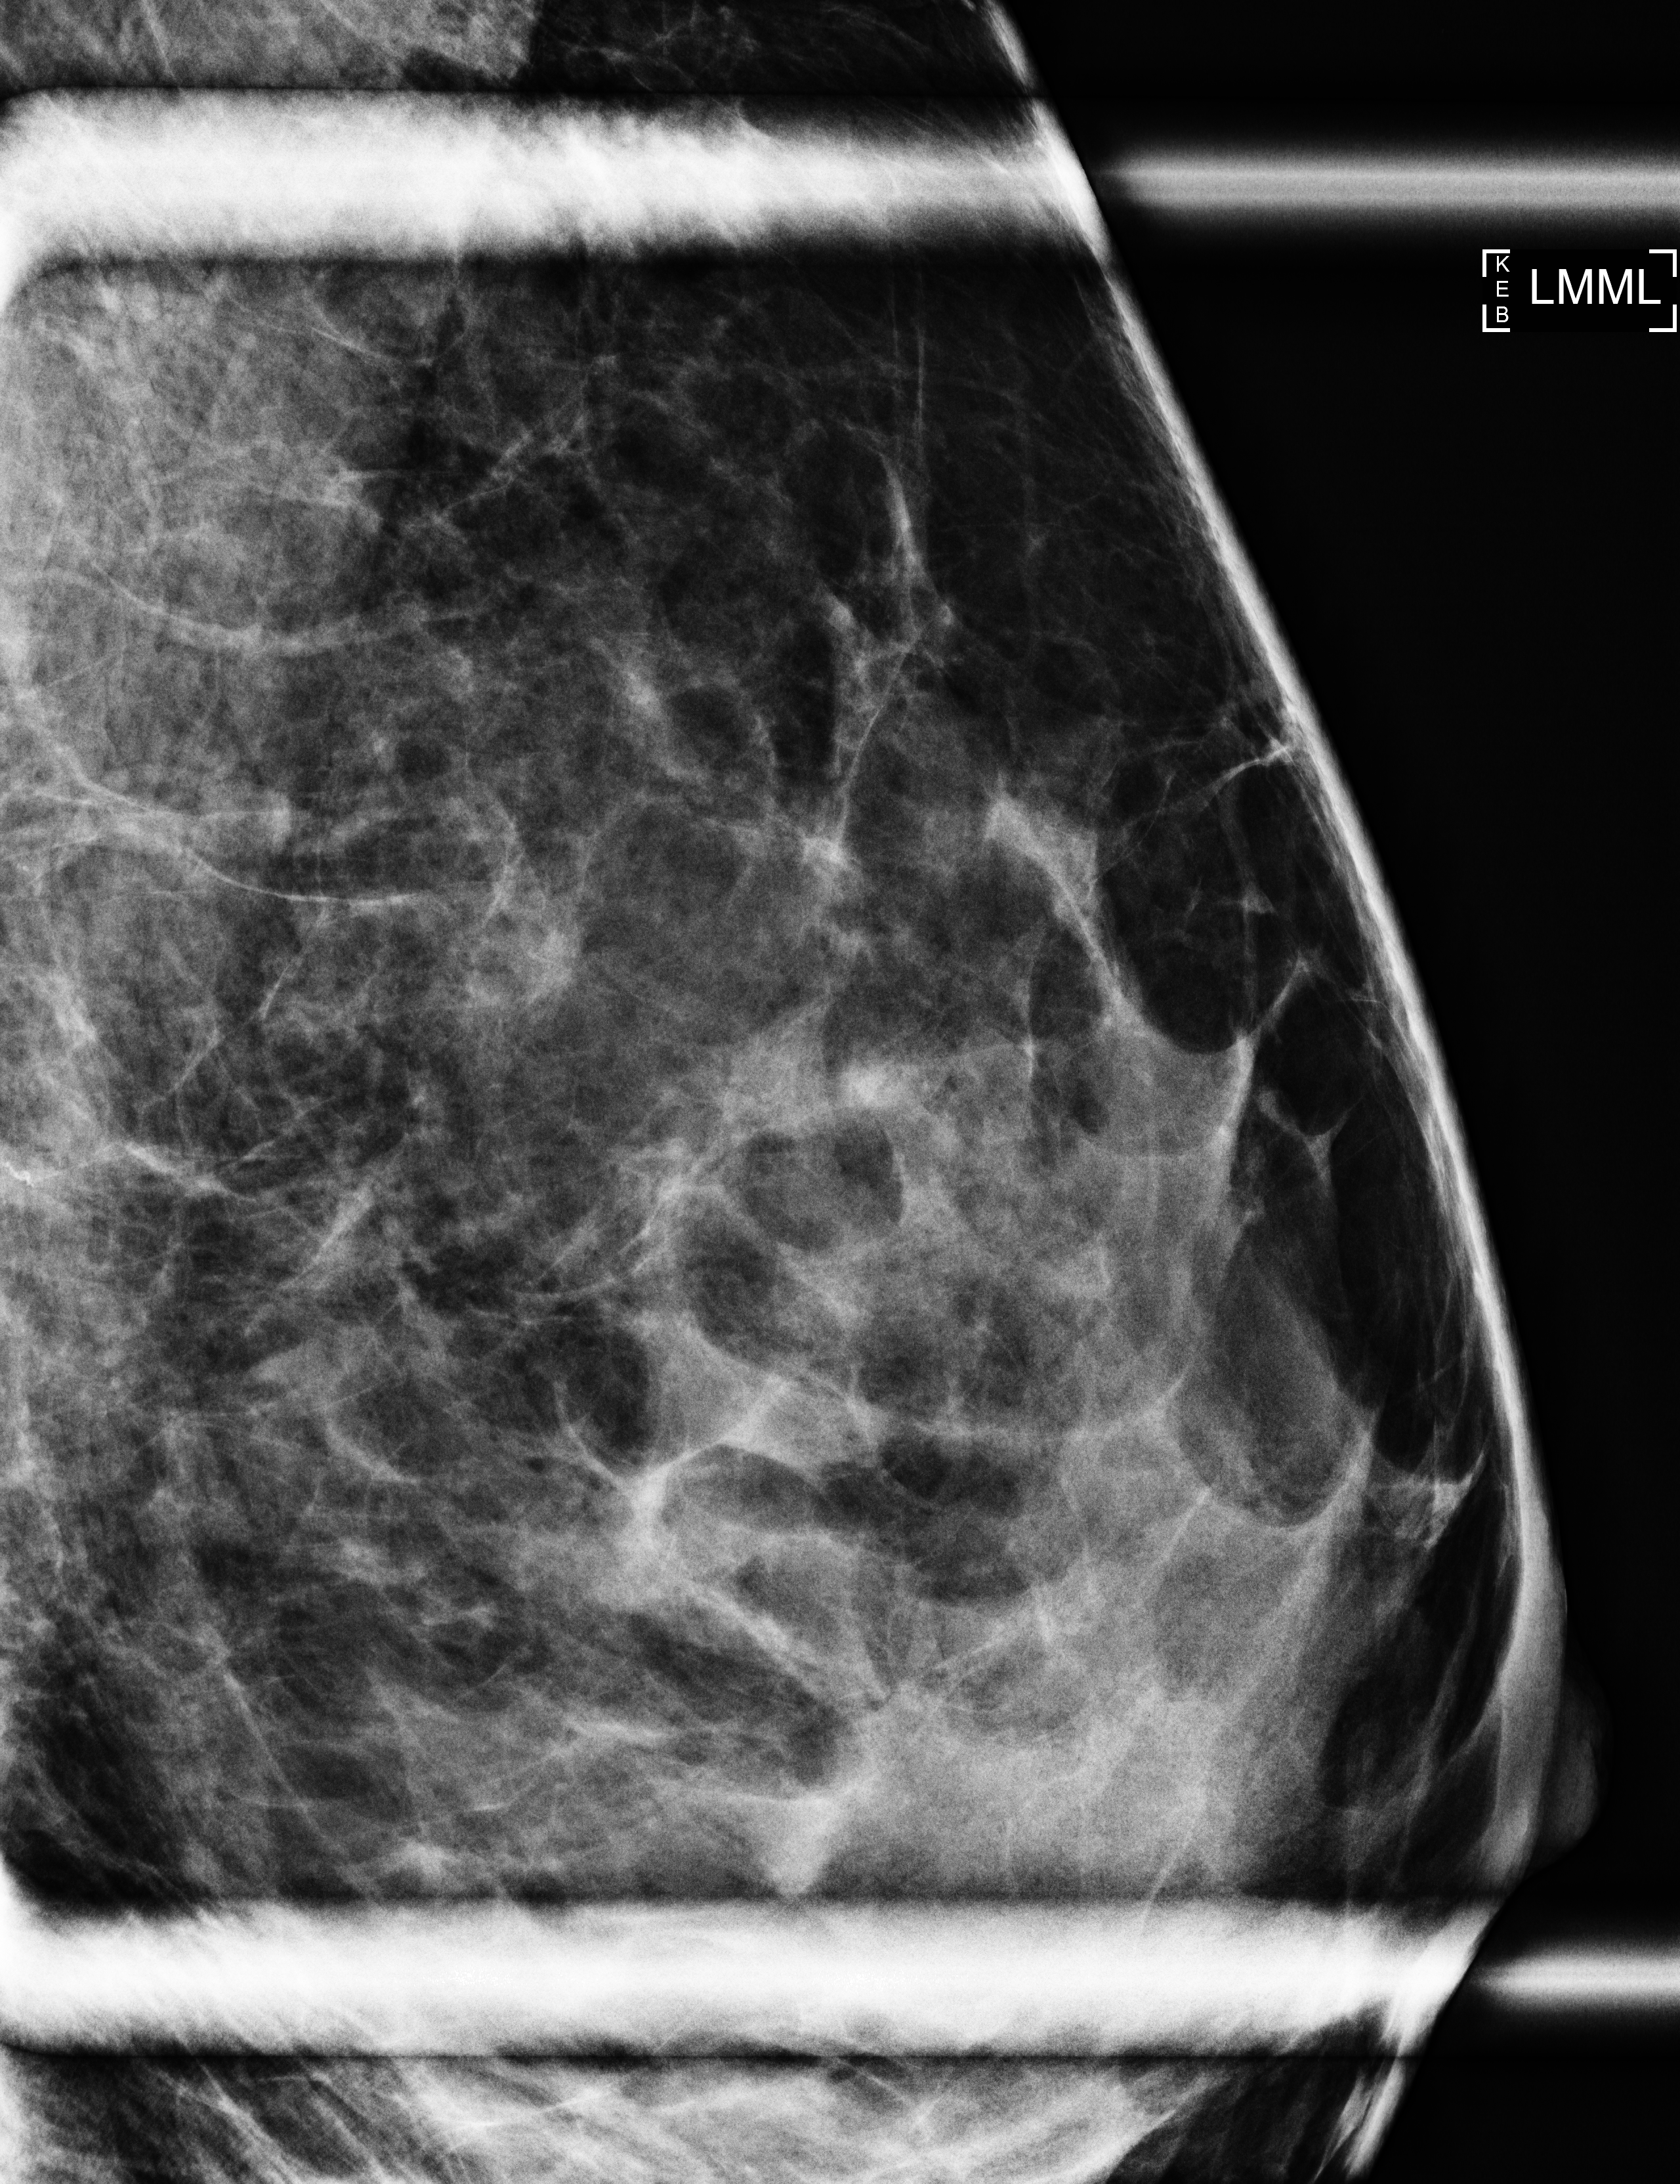
Additional (diagnostic) view, compressed breast thickness 37 mm, system: Selenia Dimensions. Female patient, age 56 years.
Image type: full-field digital mammogram. Breast: left. Projection: ML view, magnification.